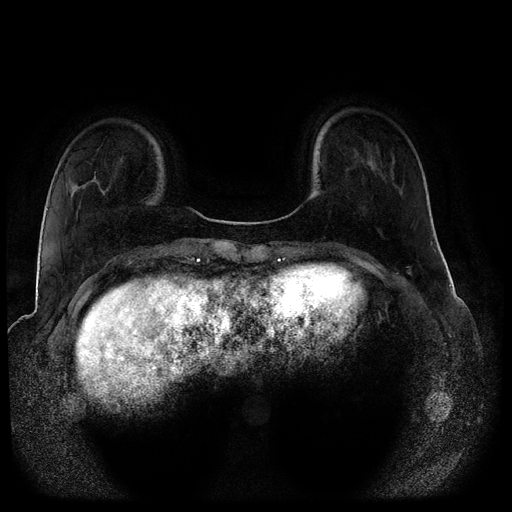
Breast MRI (dynamic contrast-enhanced, multi-phase), one axial slice. Slice 28 of 116 in the series (ordered by position). Dynamic contrast-enhanced series, time point 2 of 5 at this slice position (early post-contrast). 1.5 T. TE 2.6 ms, TR 5.3 ms. 2 mm slice thickness. 512 × 512 image matrix. Patient: female, 44 years.
Annotated regions visible in this slice (semi-automatic segmentation, software-assisted and operator-edited):
- breast lesion (labelled benign in the annotation): bounding box [x1, y1, x2, y2] px = [368, 161, 373, 166]